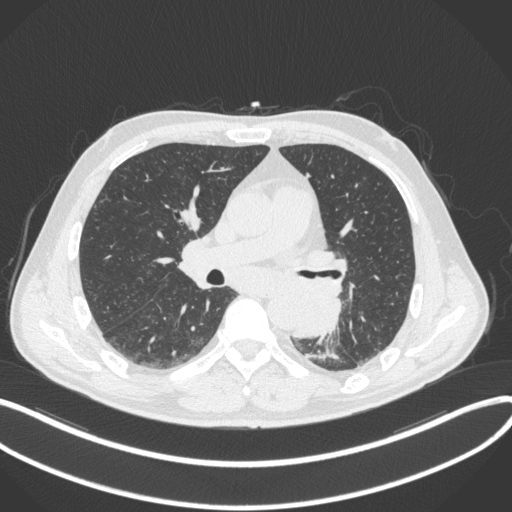
Chest CT, one axial slice; position 186 of 328 along the scan axis; 120 kVp; lung window (W 1500 / L -600 HU); 512 × 512 image matrix, field of view 400 × 400 mm. Male patient, age 59 years. From the clinical record (not read from this slice): clinical TNM (as recorded): T2a N2 M0.
Annotated regions visible in this slice (bounding box drawn by a radiologist):
- lung tumour (recorded histology: squamous cell carcinoma): bounding box [x1, y1, x2, y2] px = [283, 290, 342, 343]